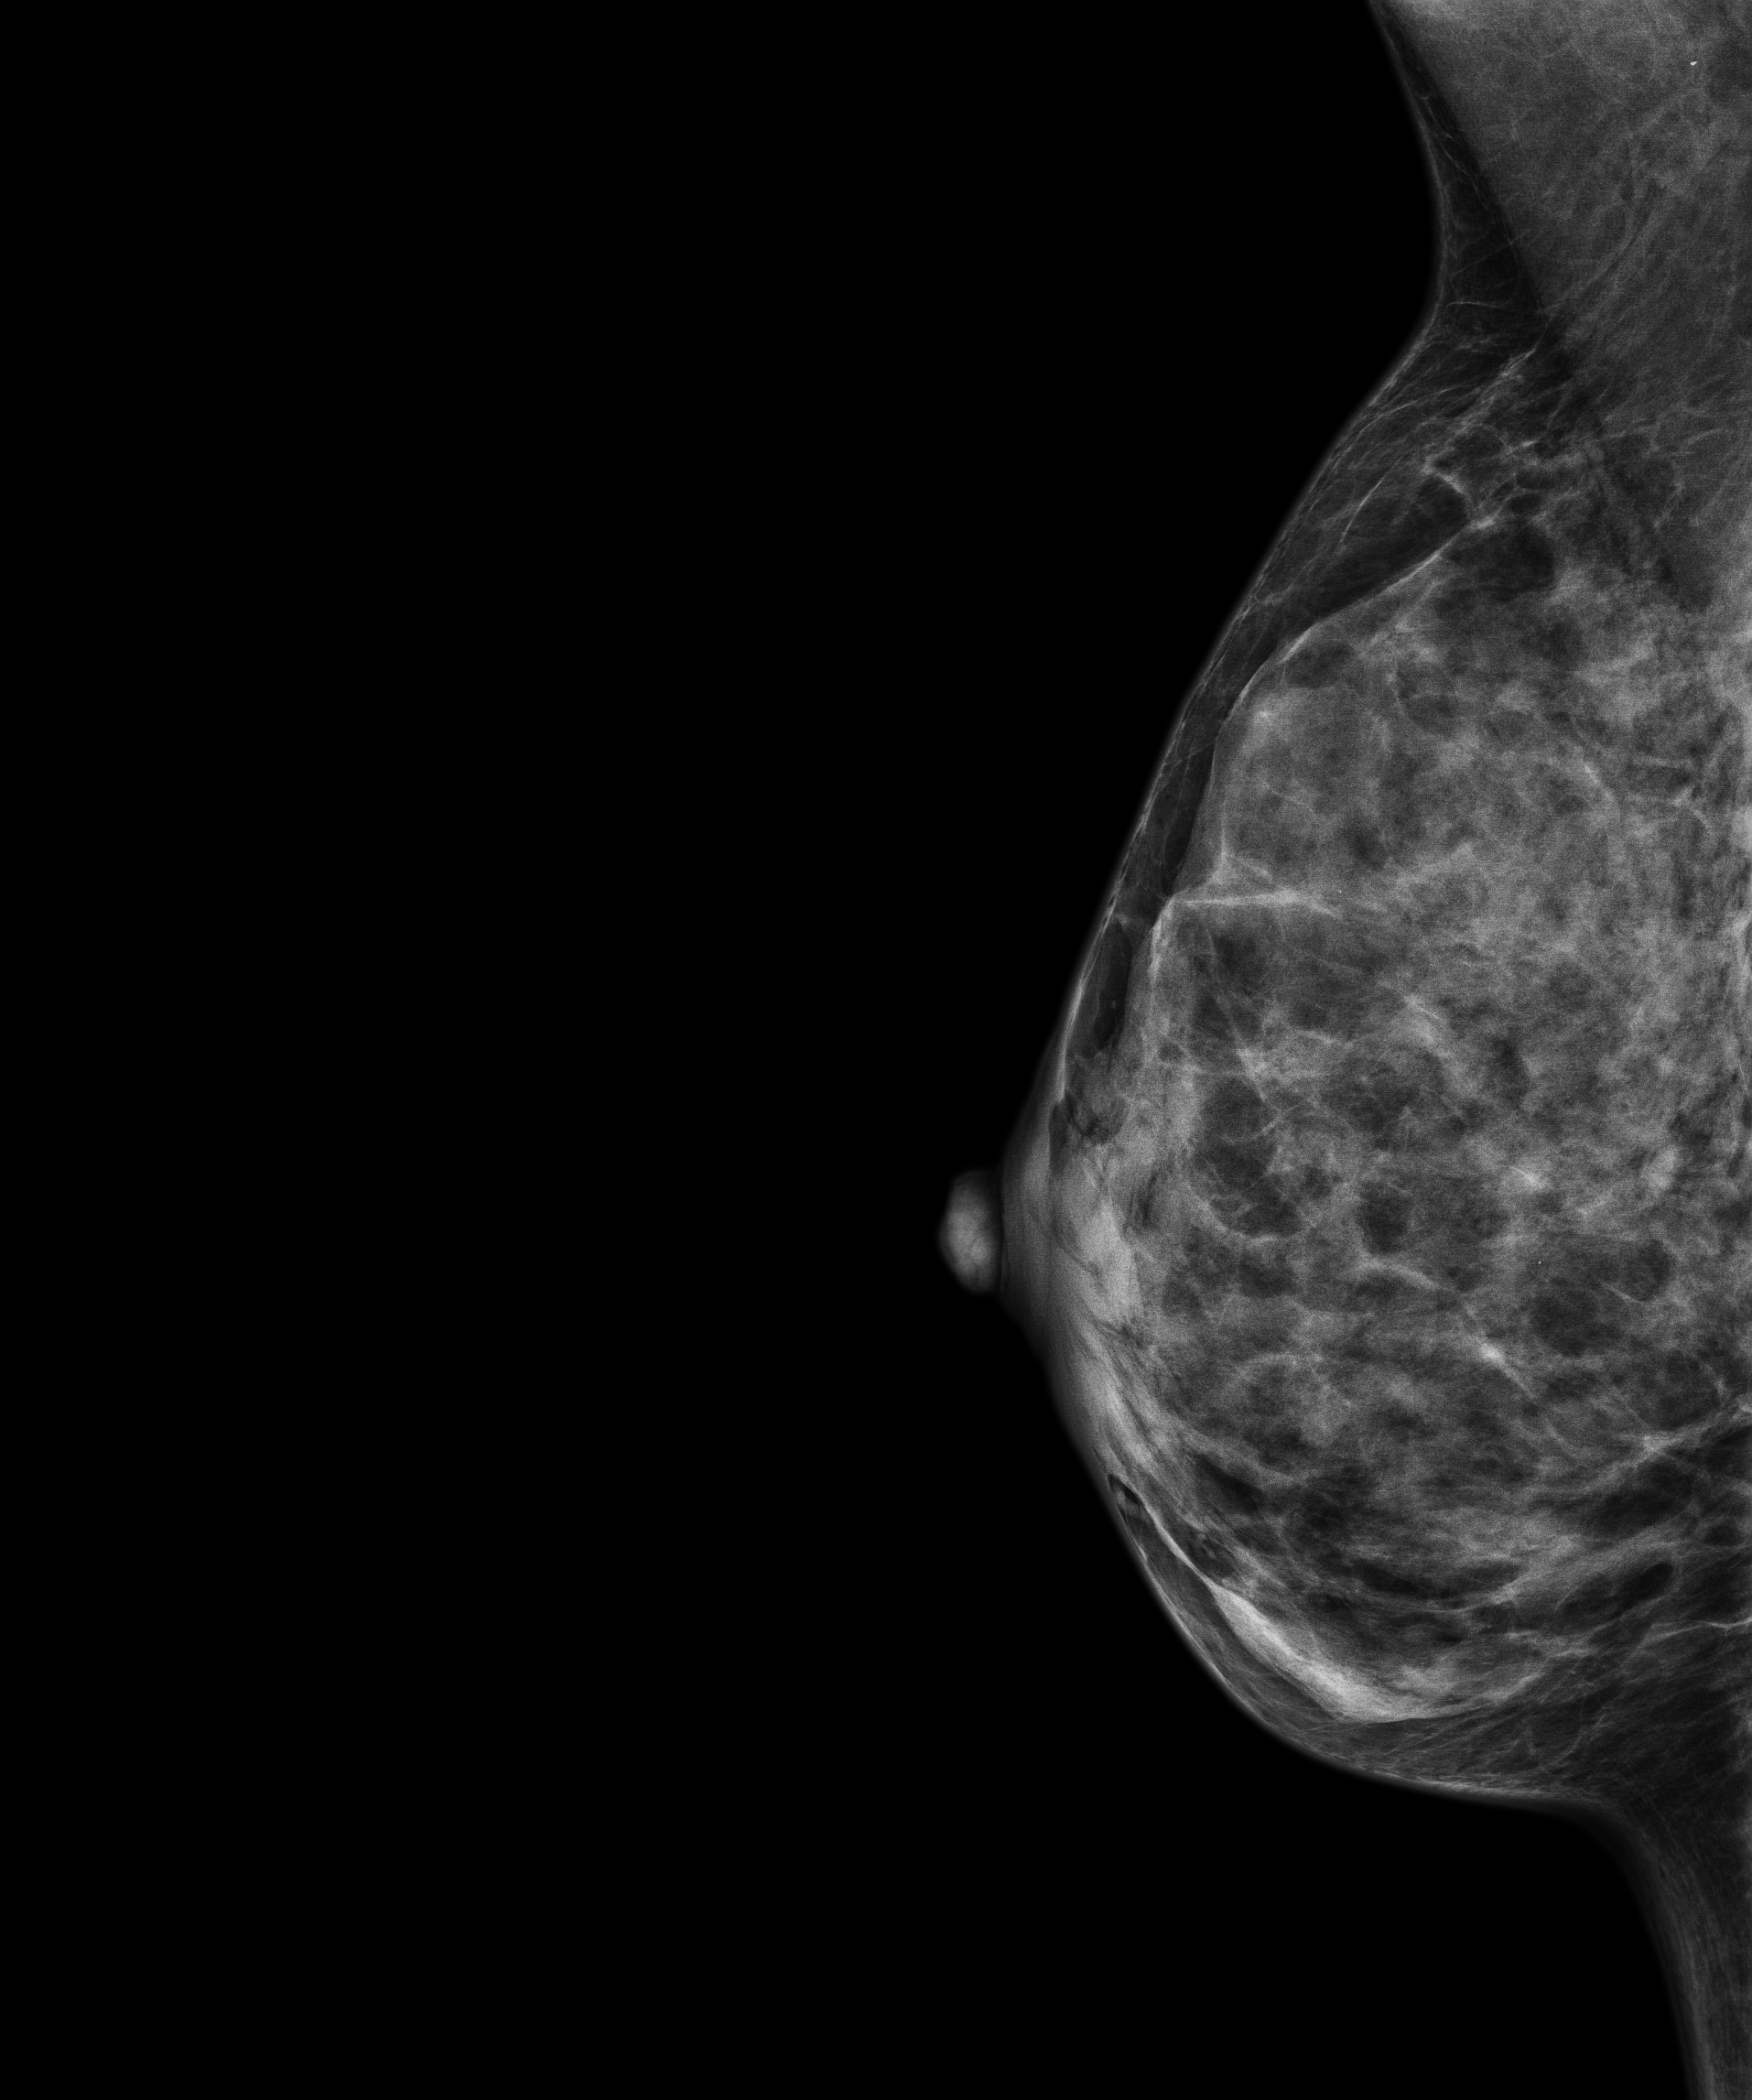
Screening examination. Female patient, age 46 years.
Image type: full-field digital mammogram. Breast: right. Projection: medio-lateral oblique projection.